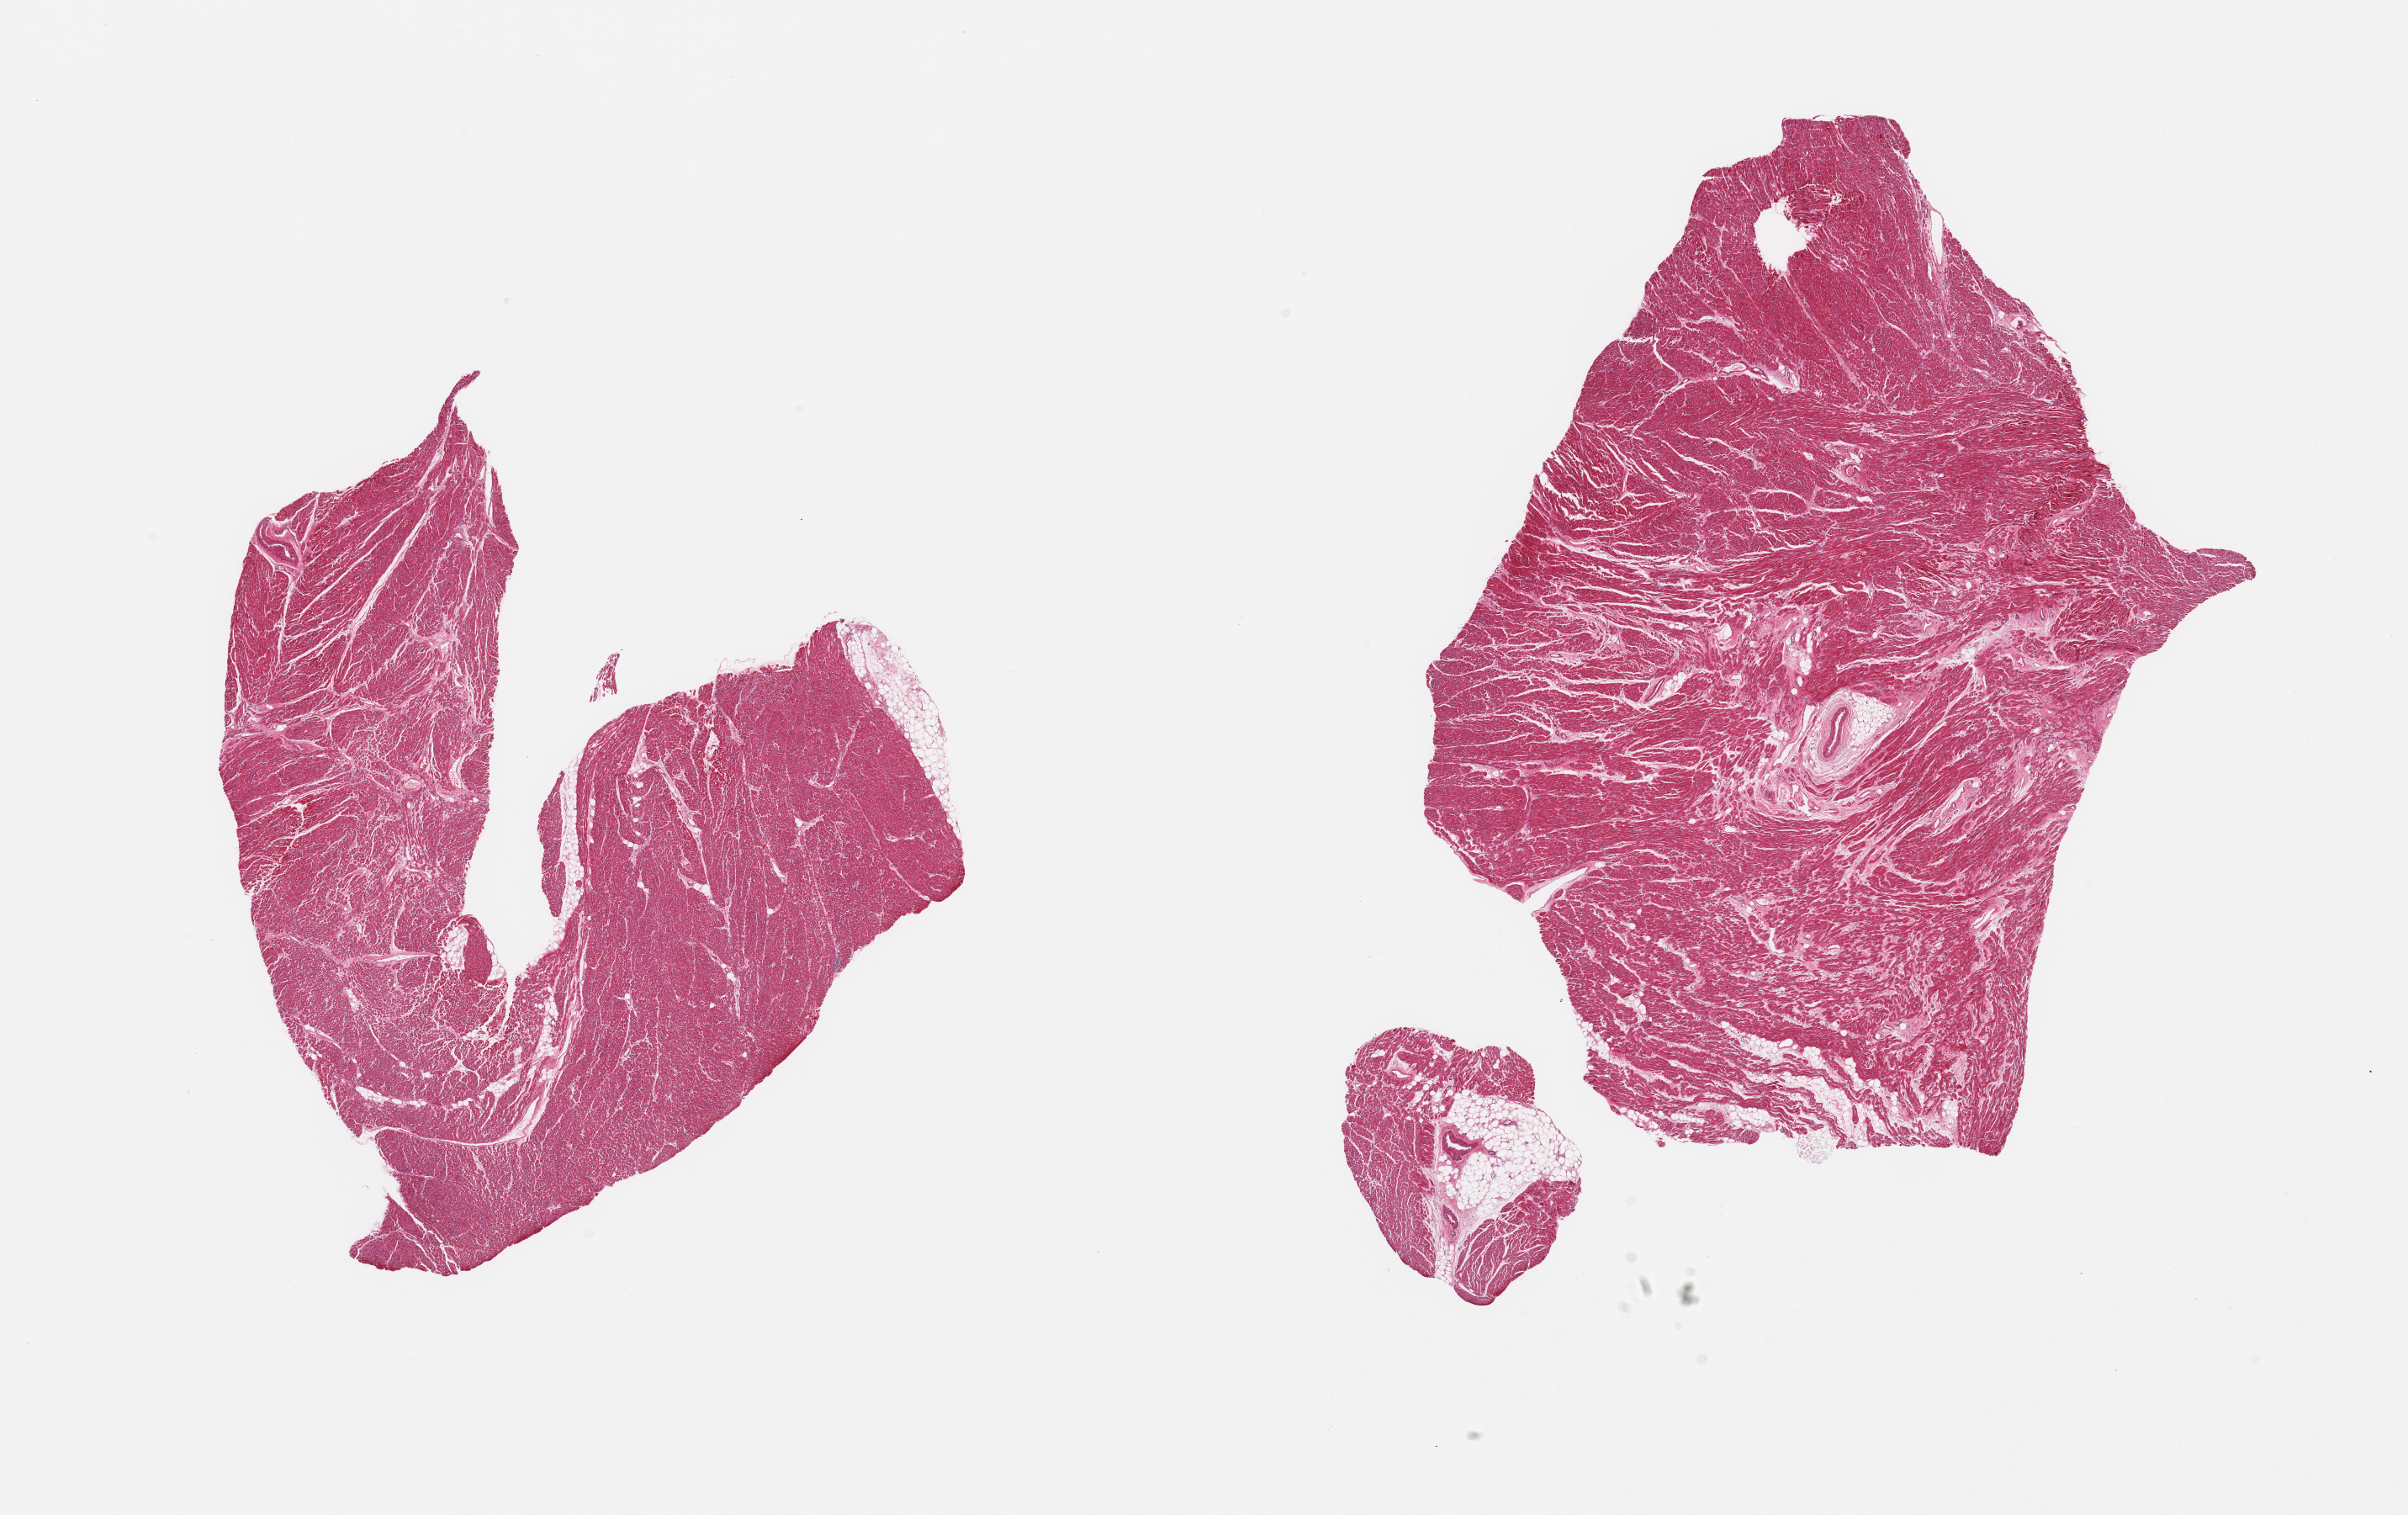
Haematoxylin and eosin whole-slide image, shown as a low-resolution overview of the whole scanned area (about 22.6 x 14.2 mm). PAXgene-fixed paraffin-embedded (PFPE) section. Section of heart (target tissue). Tissue donor sample. Donor: male.
Reviewer comment on this tissue sample: 2 pieces; no scars or necrosis; 5% internal fat.